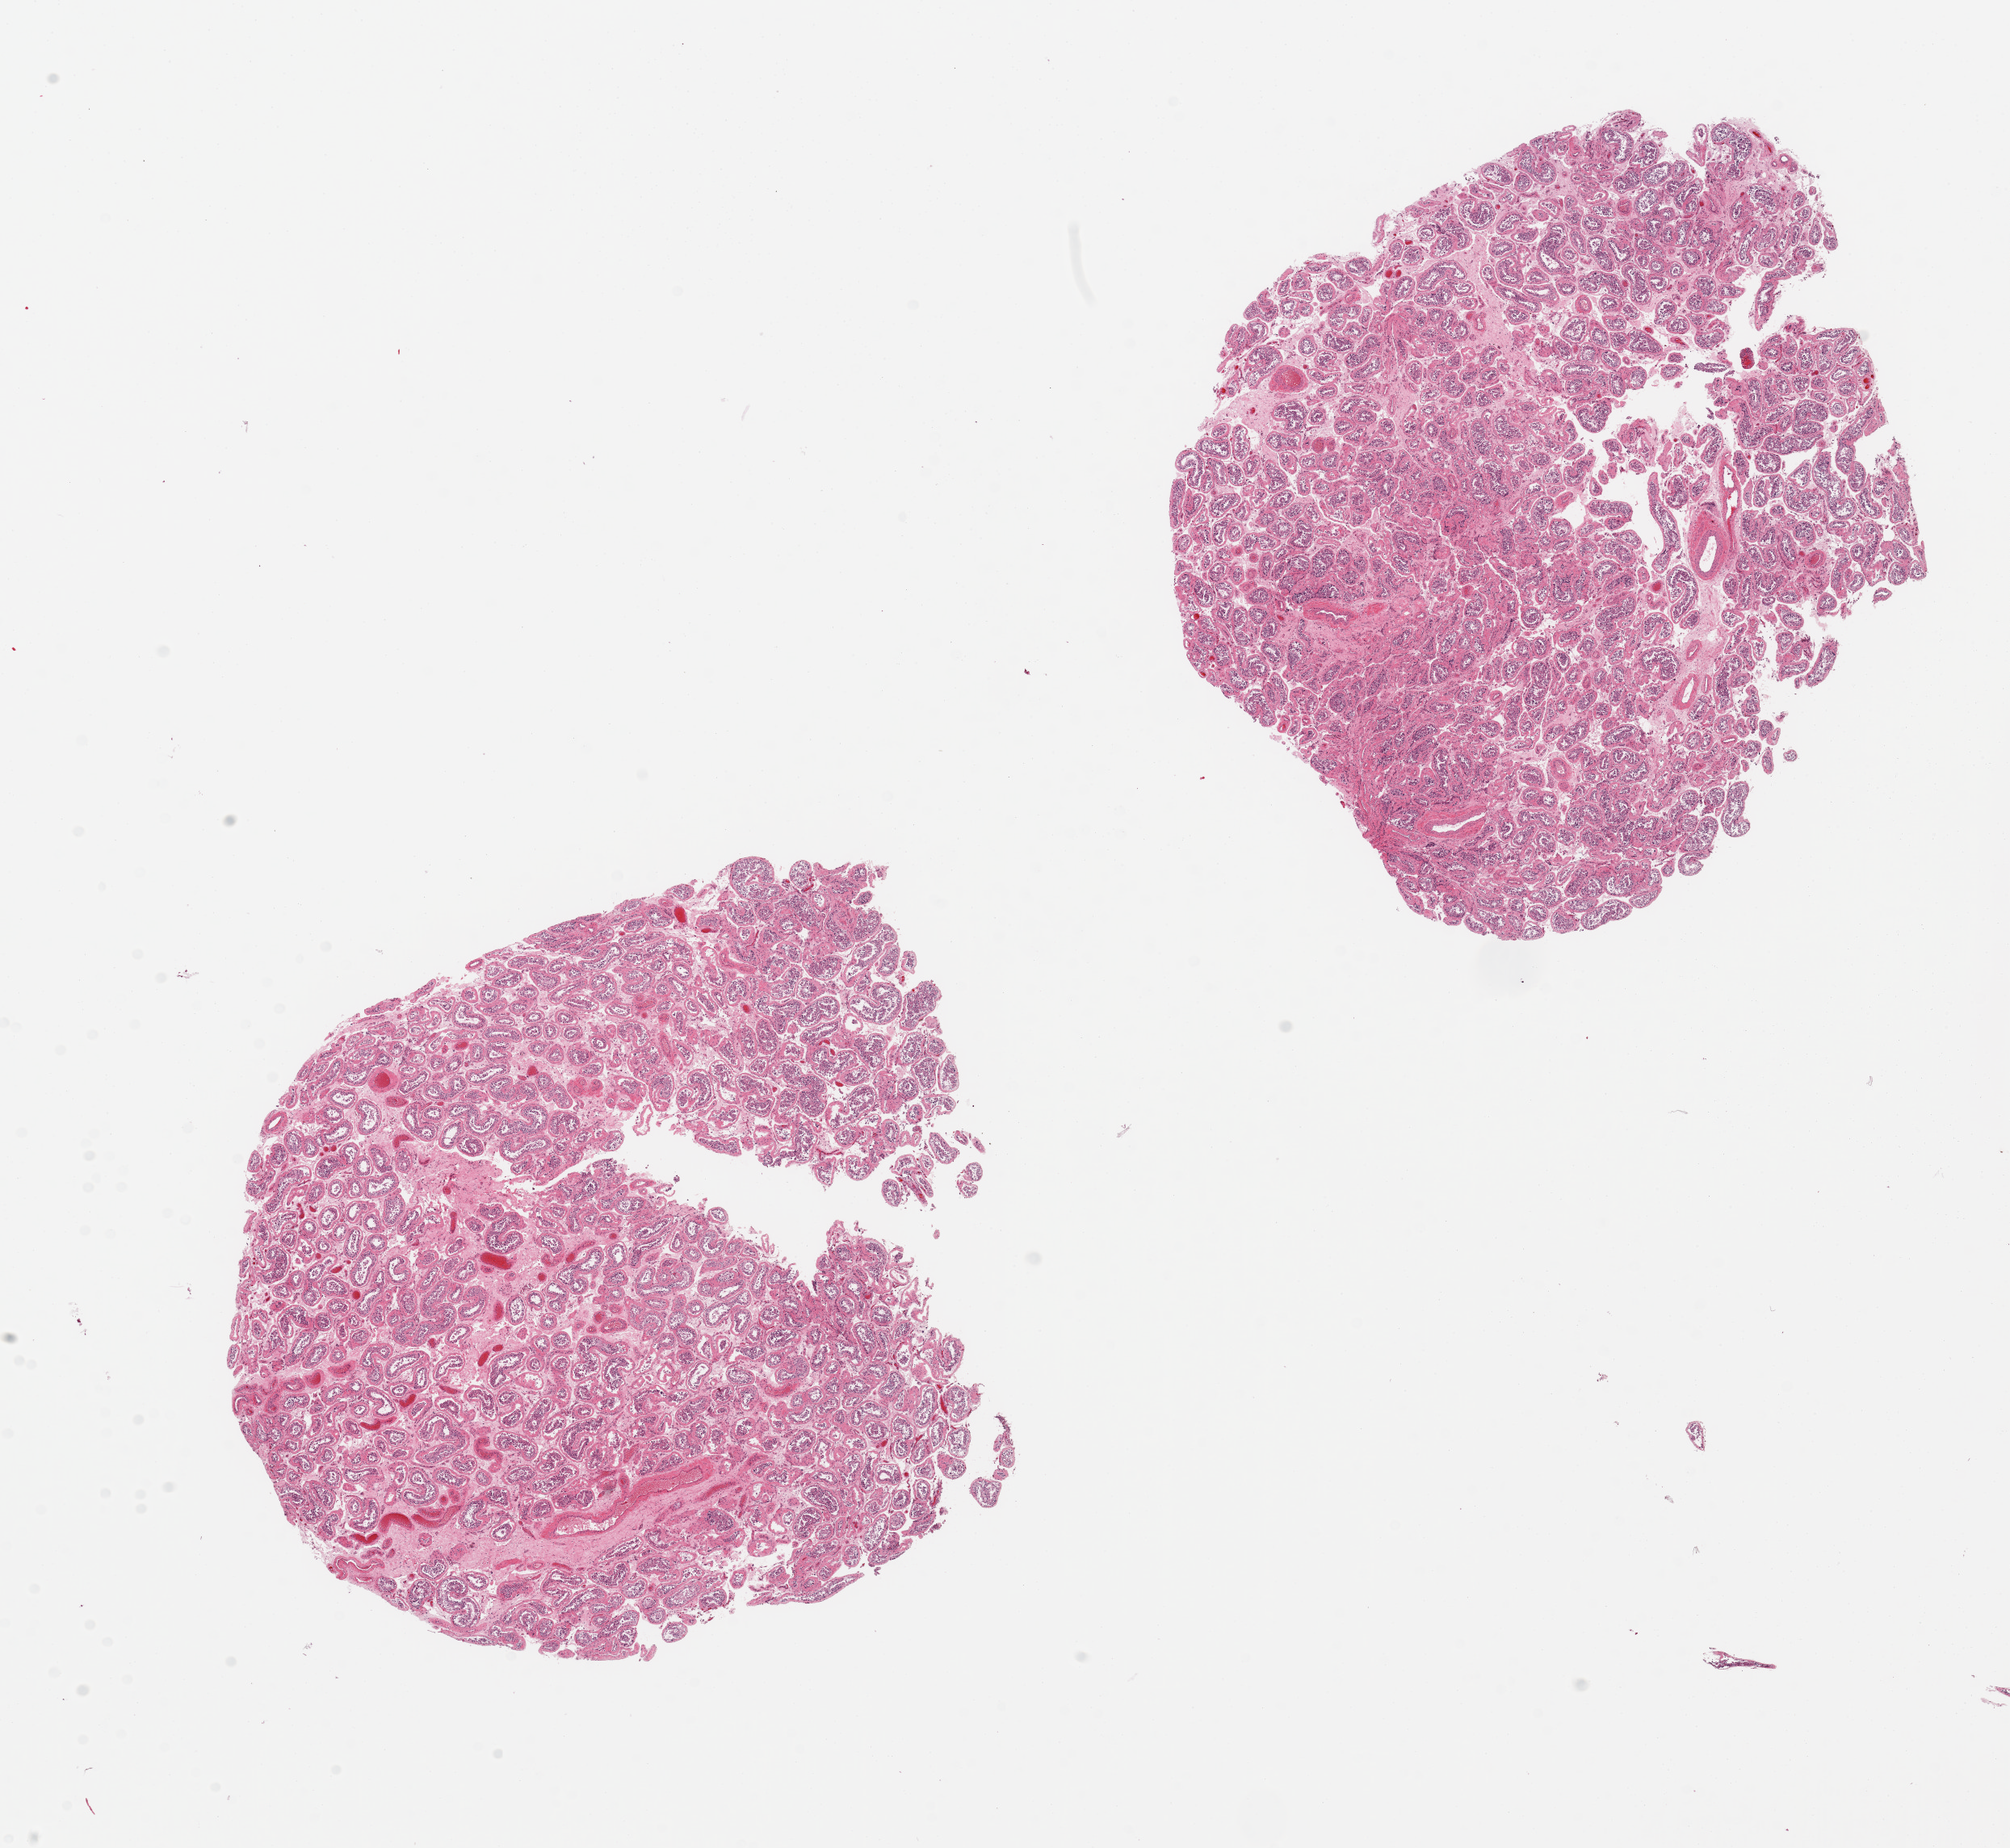
H&E whole-slide image — shown as a low-resolution overview of the whole scanned area (about 19.7 x 18.1 mm). PAXgene-fixed, paraffin-embedded tissue. Section of testis (target tissue). Tissue donor sample. Male donor.
Pathologist's review note for this sample: 2 pieces; reduced spermatogenesis.